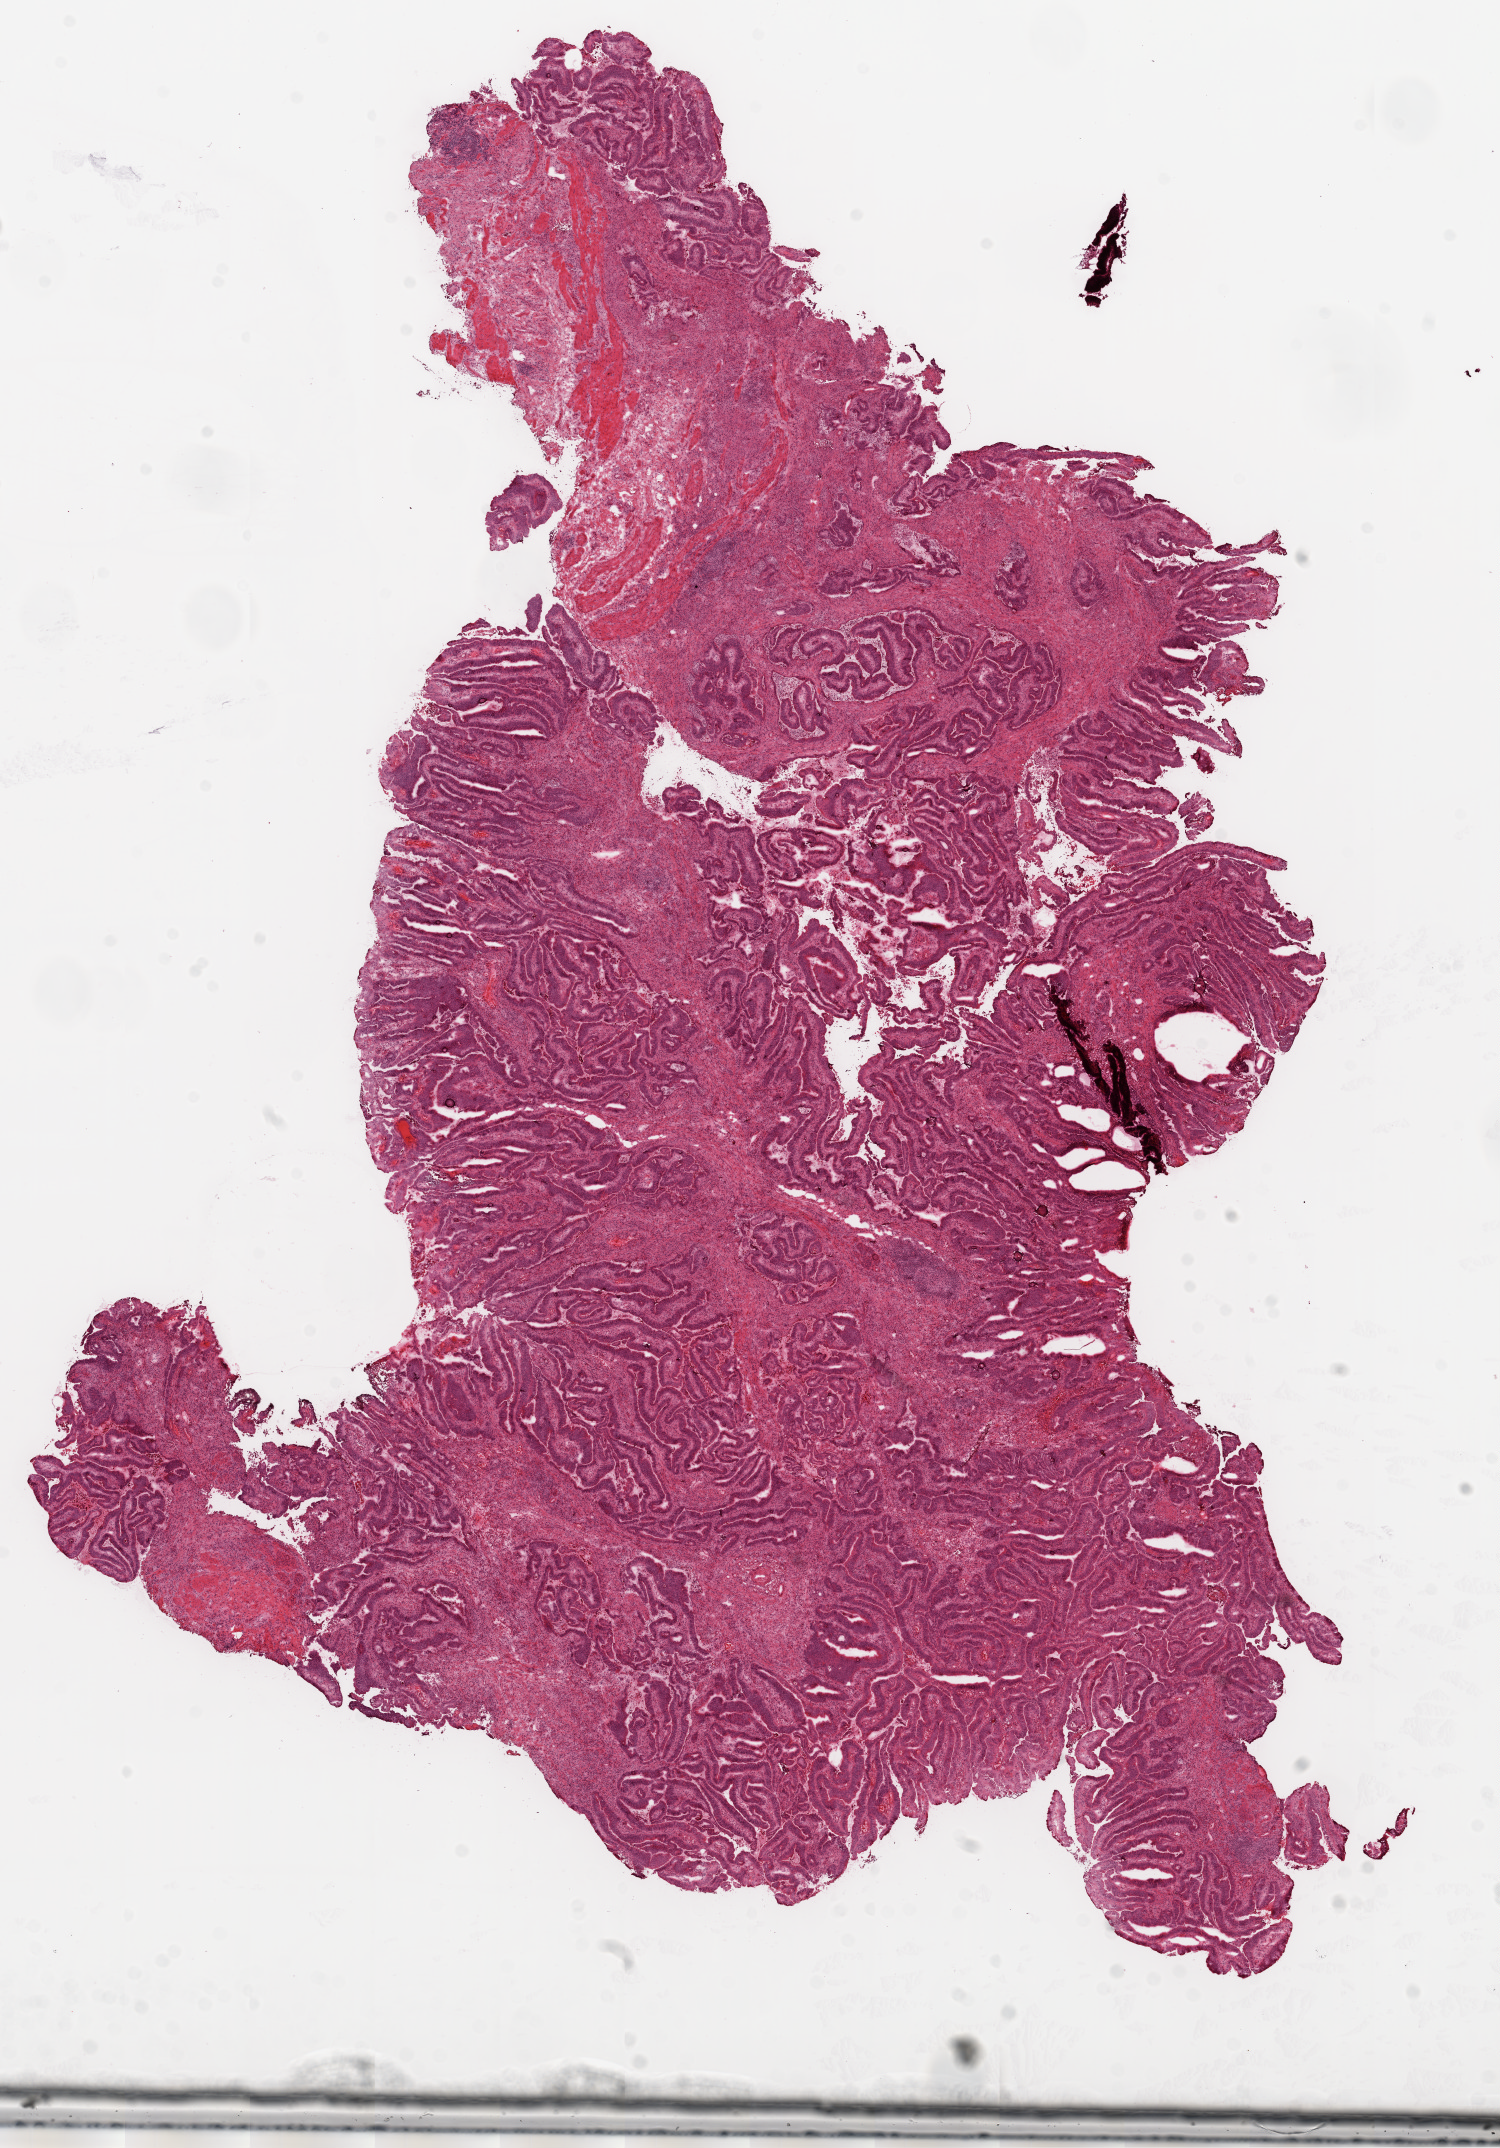
H&E-stained whole-slide image — shown as a low-resolution overview of the whole scanned area (about 12.0 x 17.2 mm, from a 20x scan). Frozen section from the top of the tissue portion. Sample: primary tumour, colon. Patient: male, age at initial diagnosis 69 years. Pathologist review of this section (percent, as recorded): tumour cells 70%, tumour nuclei 75%, normal cells 10%, stromal cells 15%, necrosis 5%.
Histologic diagnosis: Adenocarcinoma, NOS (cecum). AJCC pathologic stage: I.